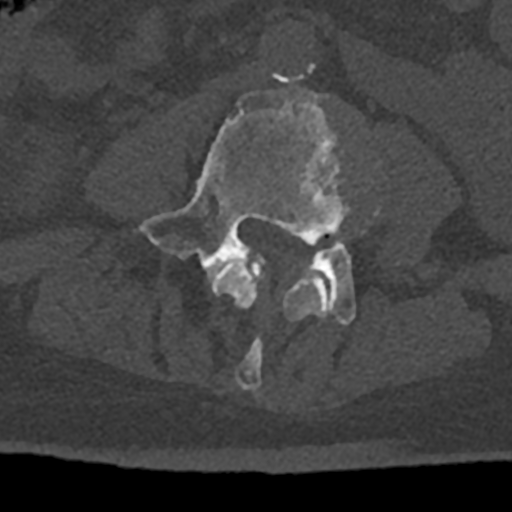
CT including the spine, one axial slice; slice 278 of 797 in the series (ordered by position); 120 kVp; bone window (W 1800 / L 400 HU); 512 × 512 image matrix, field of view 160 × 160 mm. Patient: male, 74 years. From the clinical record (not read from this slice): primary cancer: renal; vertebrae with lytic lesions (as recorded): T10, L1, L2, L3, L4, L5.
Outlined on this slice (semi-automatic segmentation, software-assisted and operator-edited):
- L3 vertebra: bounding box [x1, y1, x2, y2] px = [212, 211, 378, 390]
- L4 vertebra: [139, 88, 366, 325]